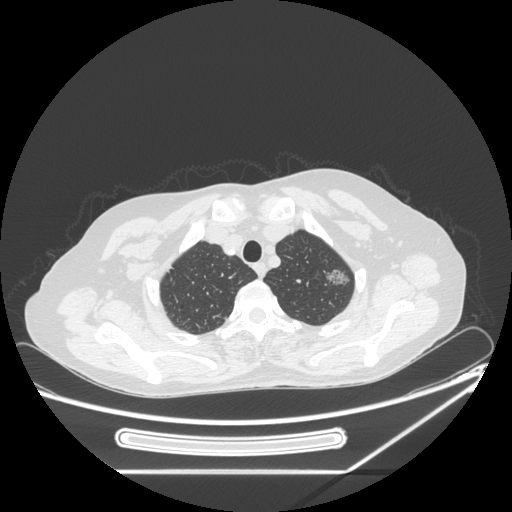
Chest CT, one axial slice. Slice 208 of 250 in the series (ordered by position). Reconstruction kernel STANDARD. 120 kVp. Lung window (W 1500 / L -600 HU). 512 × 512 image matrix, field of view 409 × 409 mm. Female patient, age 57 years. From the clinical record (not read from this slice): clinical TNM (as recorded): T1c N0 M0.
Annotated regions visible in this slice (bounding box drawn by a radiologist):
- lung tumour (recorded histology: adenocarcinoma): bounding box (x1, y1, x2, y2) in pixels: (322, 265, 359, 296)